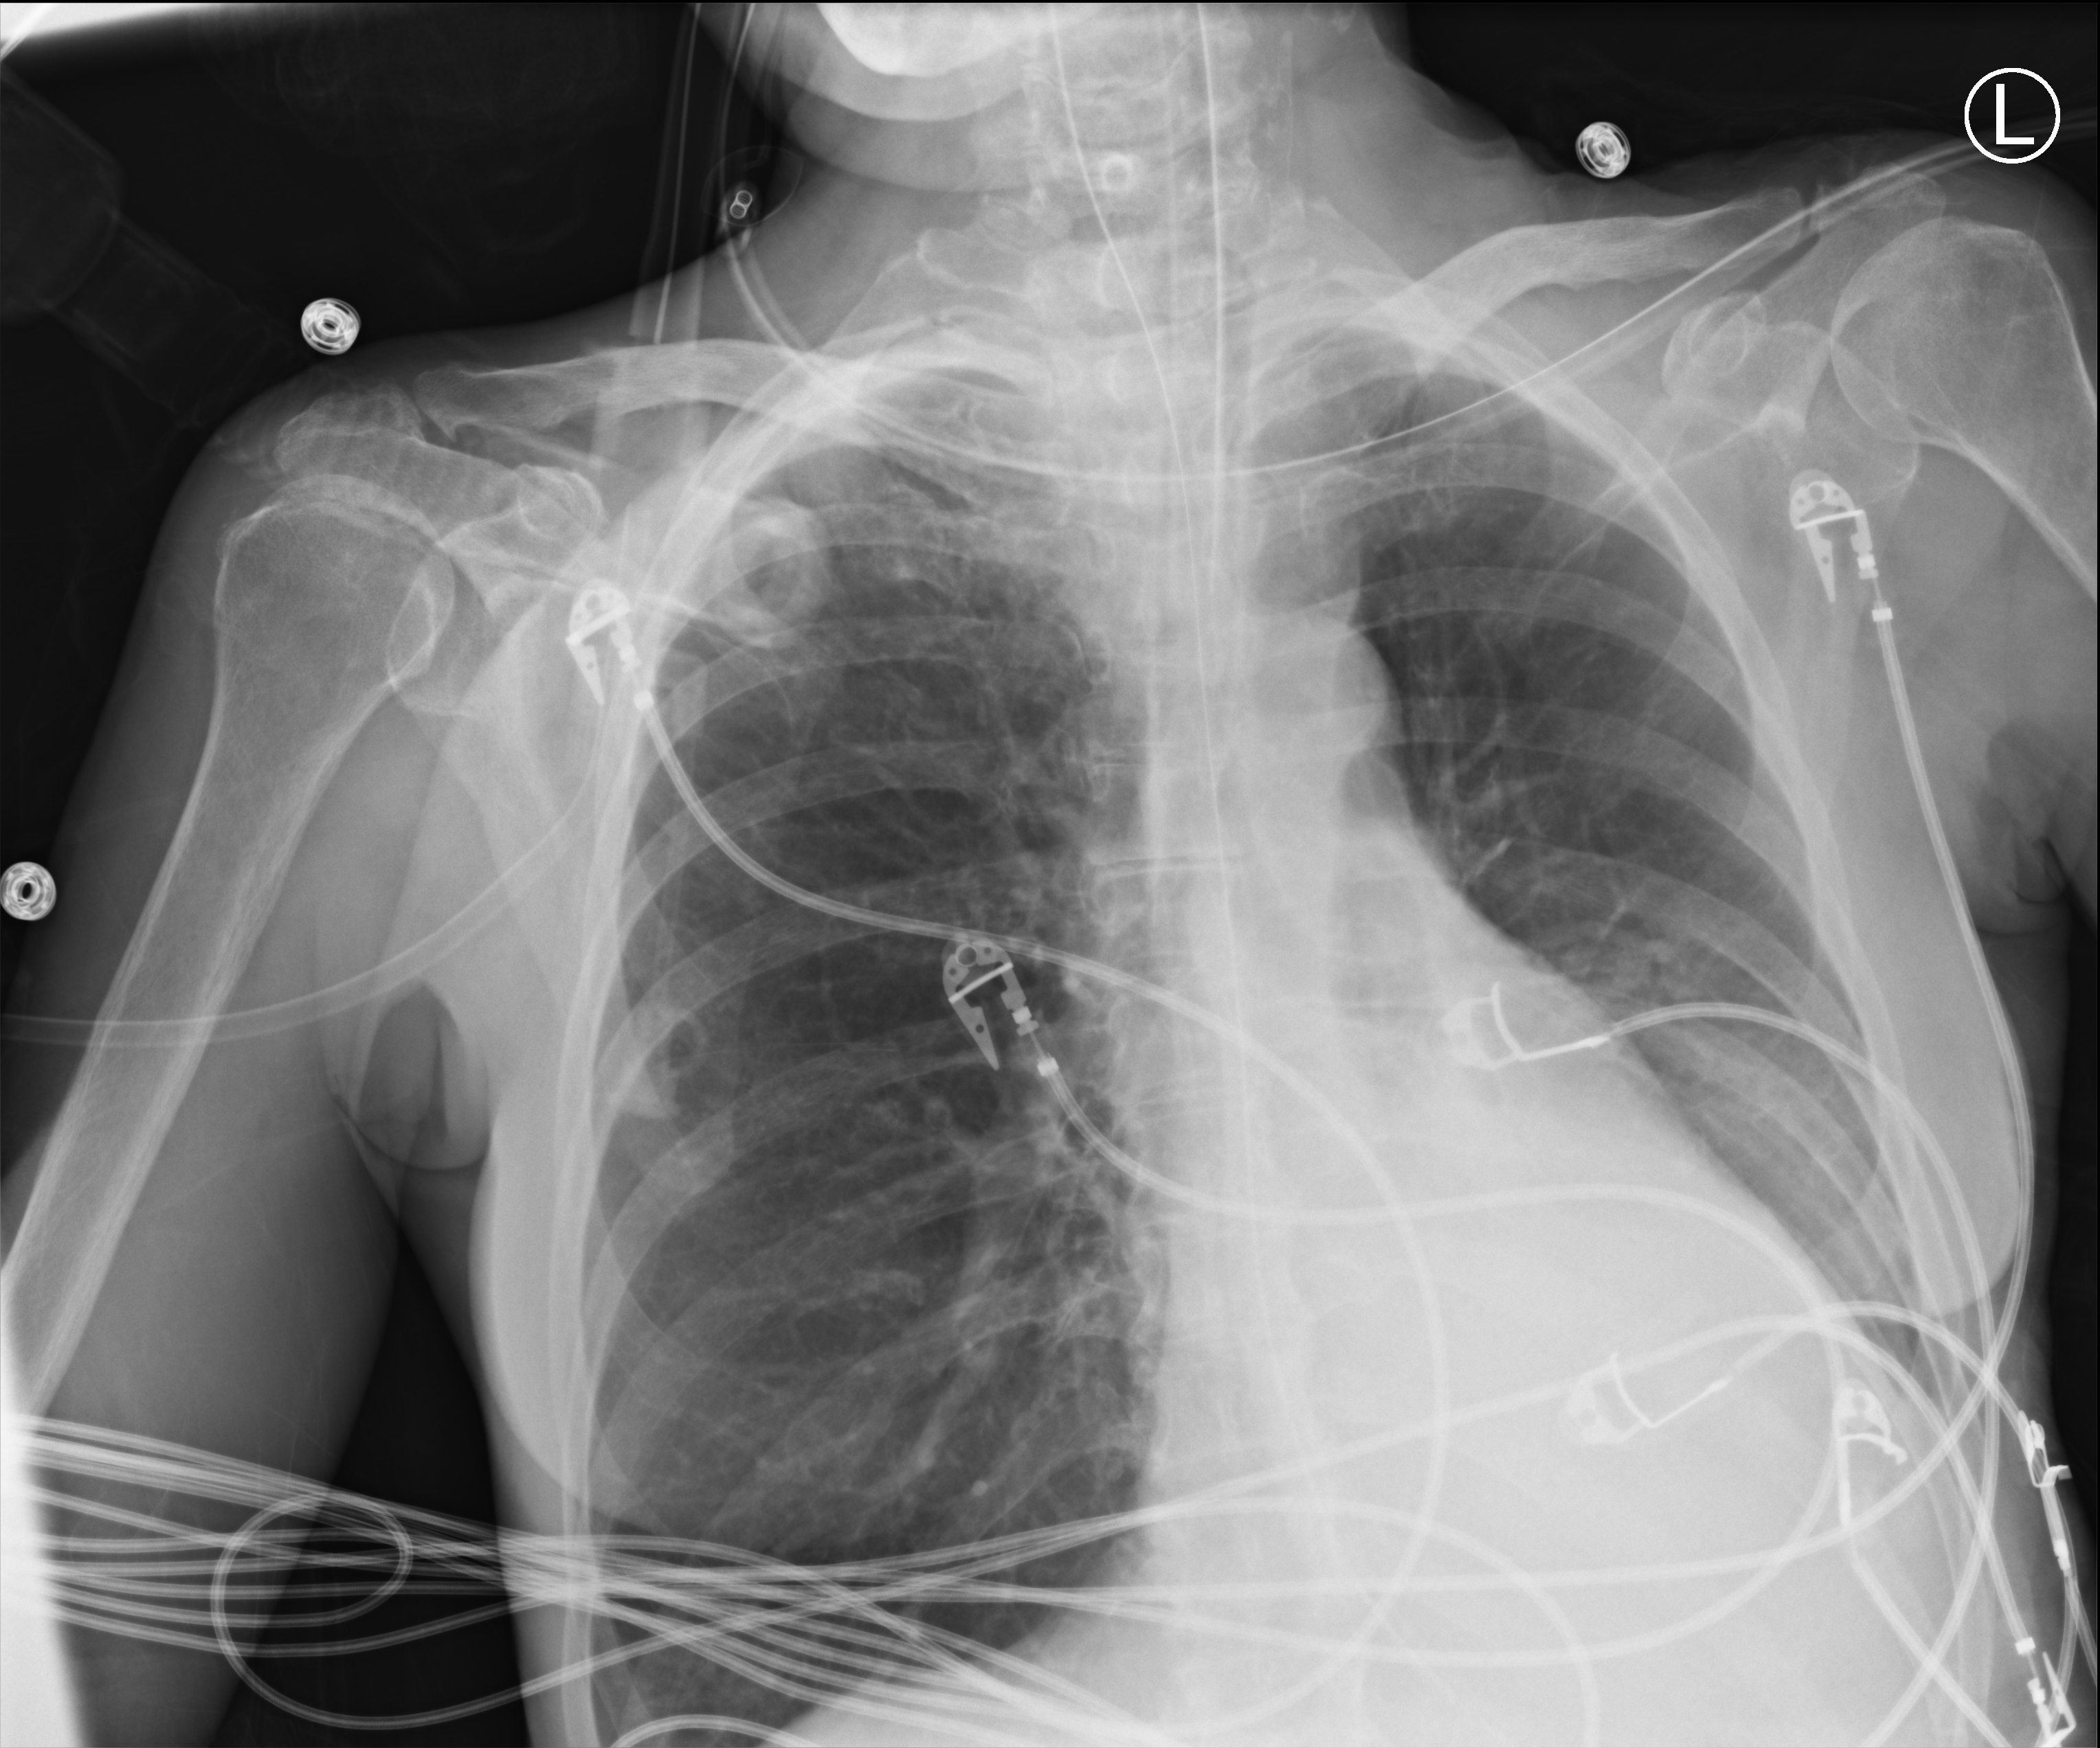
Chest X-ray (portable), anteroposterior (AP) projection. Female patient hospitalised with COVID-19, age 60–74 years.
Admission-level facts for this patient (not findings on this image; timing relative to this image not recorded):
- admitted to intensive care during this hospital stay: yes
- mechanically ventilated during this hospital stay: yes